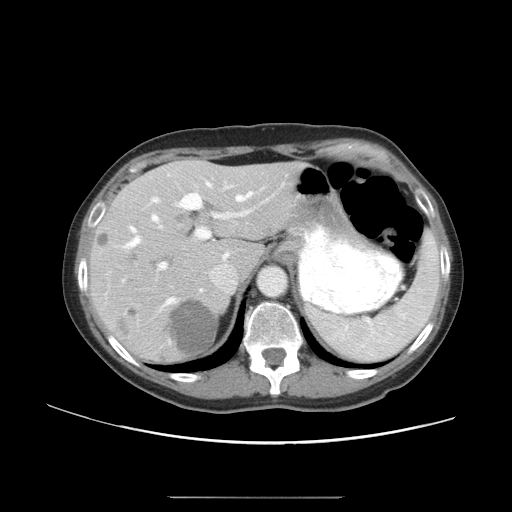
Contrast-enhanced abdominal CT, one axial slice. Reconstruction kernel STANDARD. Intravenous contrast given. Soft-tissue window (W 400 / L 40 HU). 5 mm slice thickness. 512 × 512 image matrix, field of view 389 × 389 mm. Female patient, age 58 years. From the clinical record (not read from this slice): diagnosis: colorectal cancer liver metastases, imaged before liver resection; multiple liver metastases: yes; largest metastasis: 7.3 cm.
Structures marked on this image (outlined manually by an expert reader):
- hepatic veins: bounding box (x1, y1, x2, y2) in pixels: (126, 181, 264, 306)
- liver: (93, 161, 293, 359)
- planned liver remnant (the part of the liver to remain after resection): (171, 161, 293, 272)
- portal vein (with intrahepatic branches): (151, 181, 284, 269)
- liver metastasis: (171, 301, 217, 354)
- liver metastasis: (176, 214, 200, 224)
- liver metastasis: (101, 236, 109, 247)
- liver metastasis: (98, 234, 107, 245)